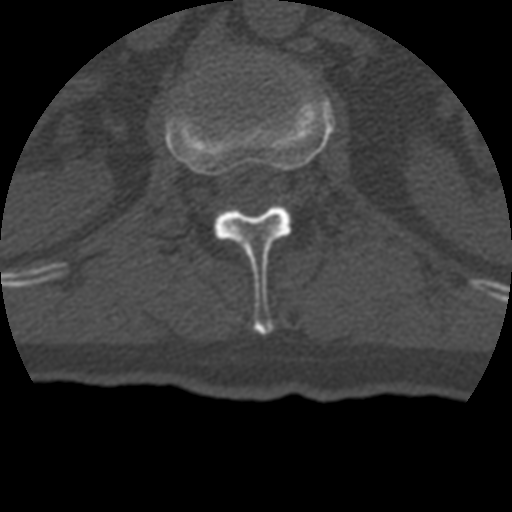
CT including the spine, one axial slice. Bone window (W 1800 / L 400 HU). 512 × 512 image matrix, field of view 160 × 160 mm. Patient age 69 years. From the clinical record (not read from this slice): primary cancer: prostate.
Annotated regions visible in this slice (semi-automatically segmented with operator editing):
- L1 vertebra: bounding box <165,89,335,334> (left, top, right, bottom; pixels)